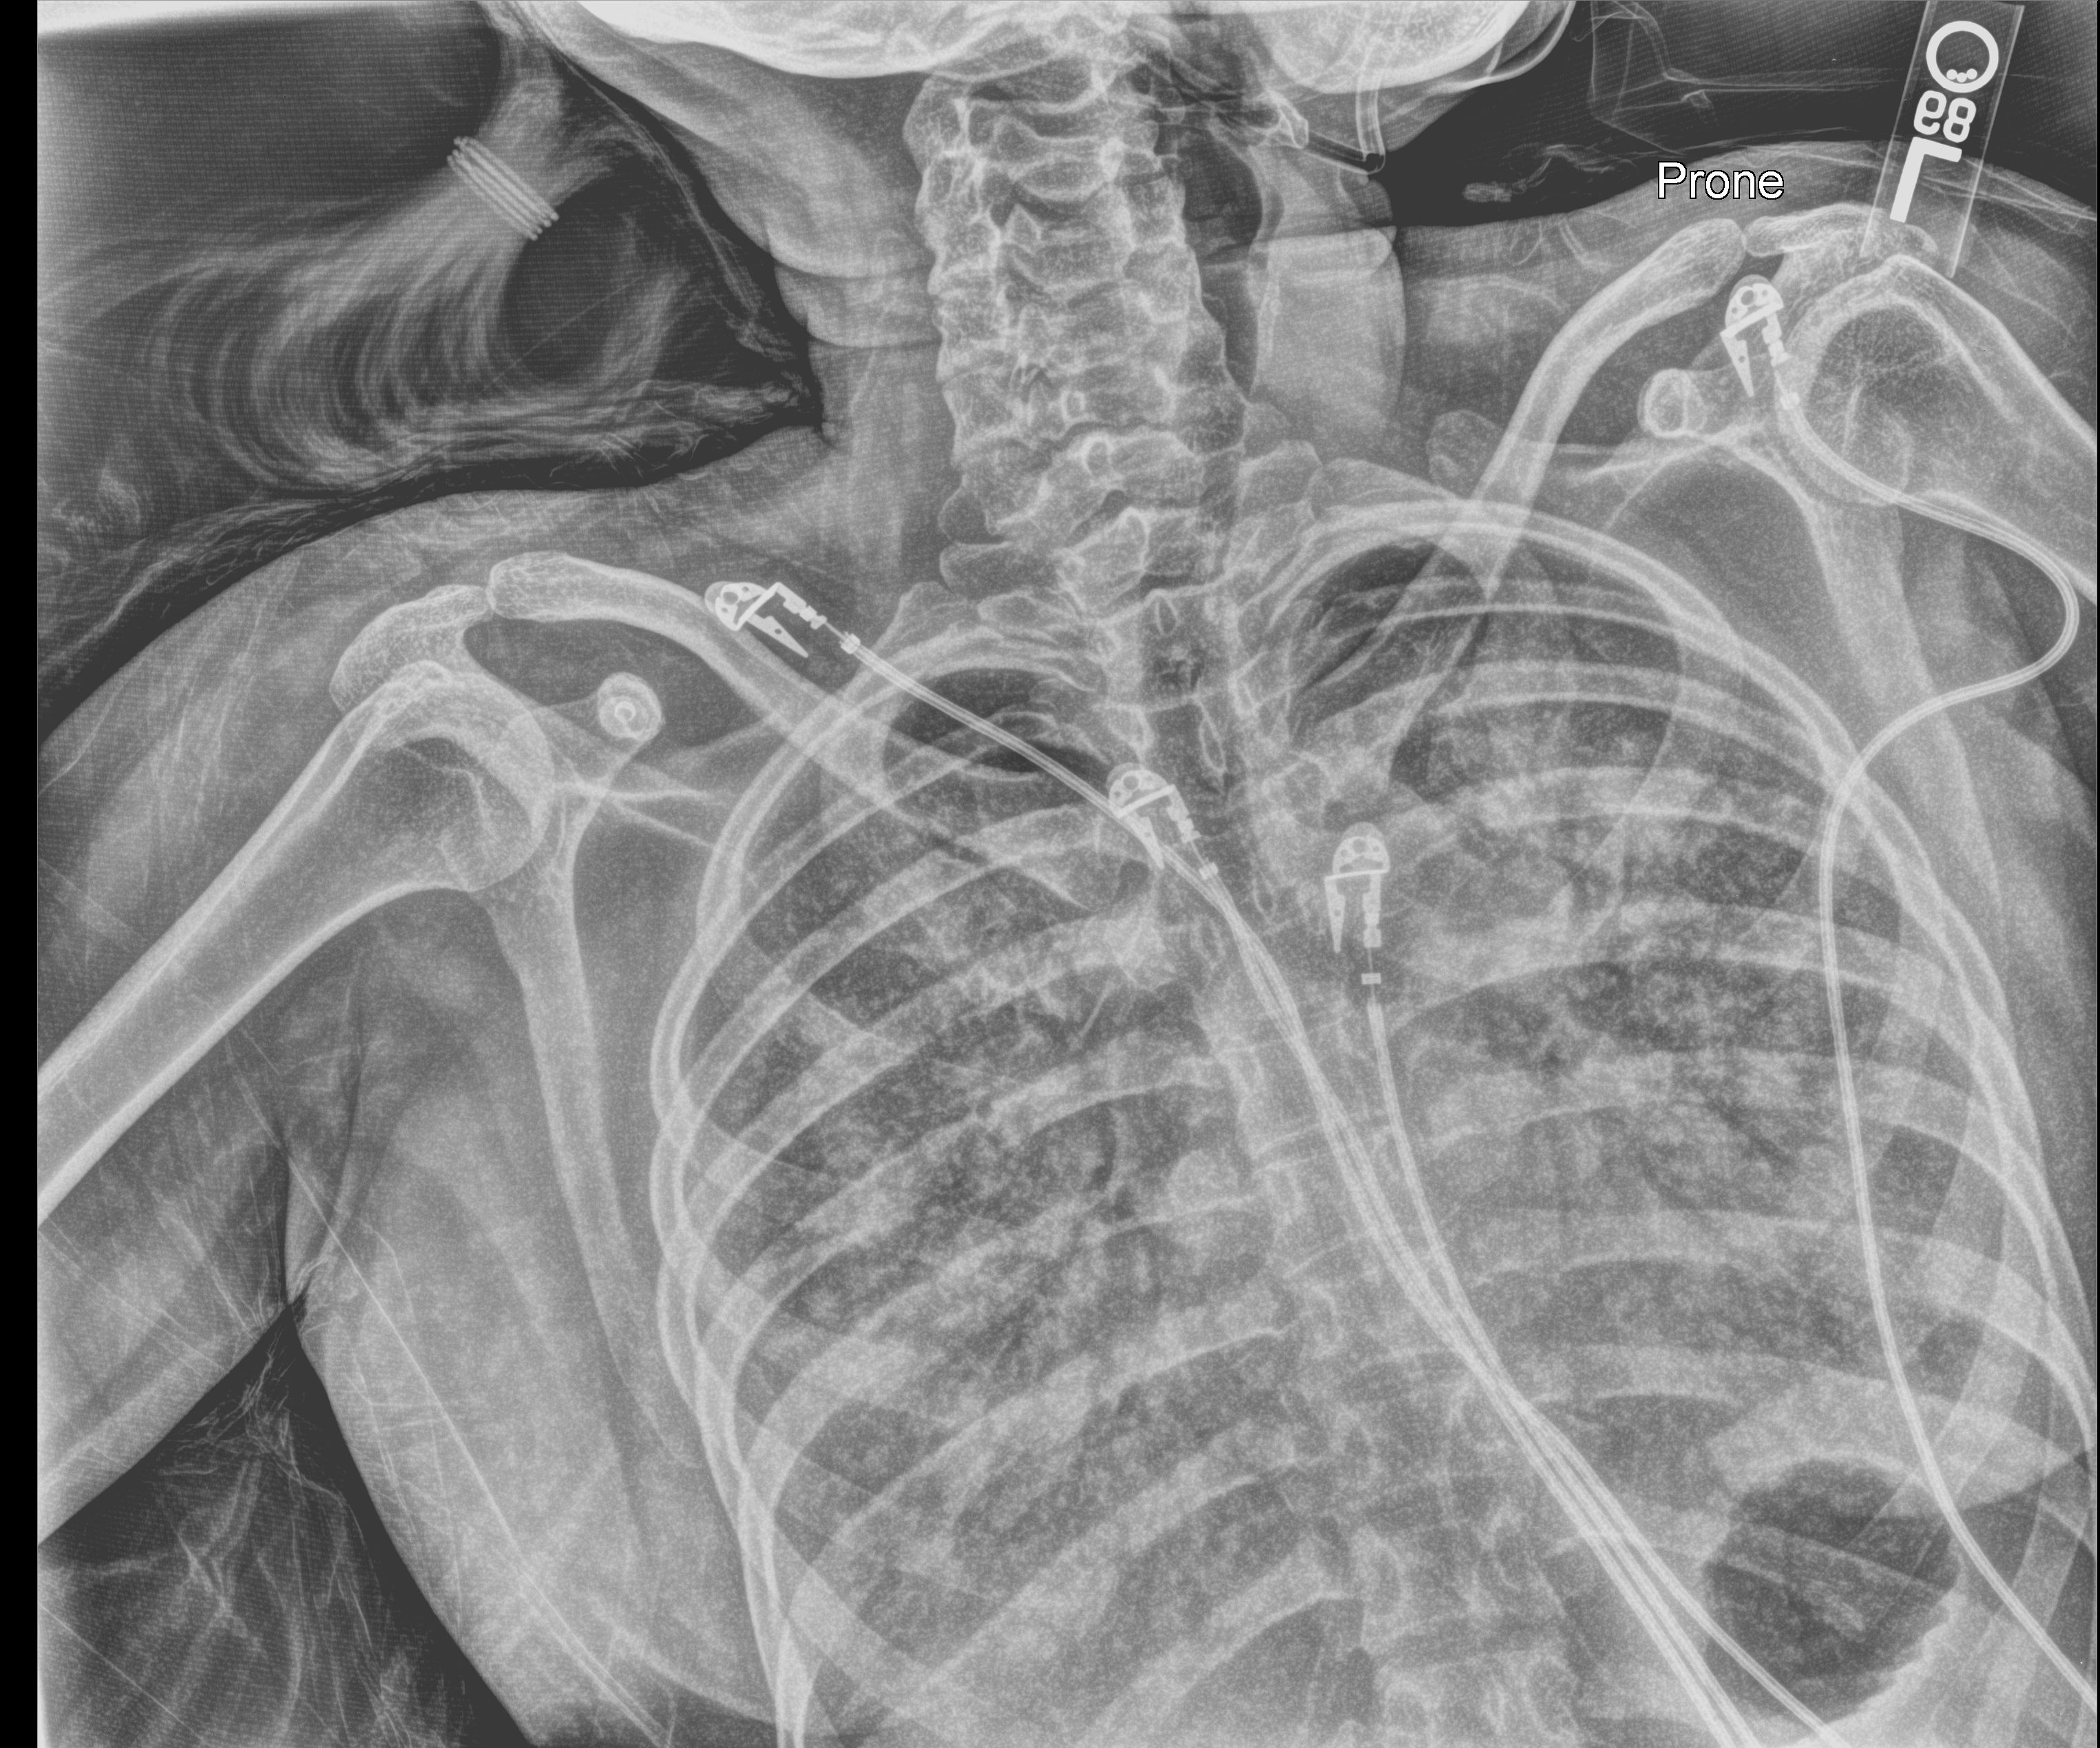
Bedside chest radiograph (computed radiography); anteroposterior (AP) projection. Adult patient hospitalised with COVID-19, age 18–59 years.
From the hospital-stay record, not from the radiograph (when in the stay this image was taken is not recorded):
- diabetes (admission record): no